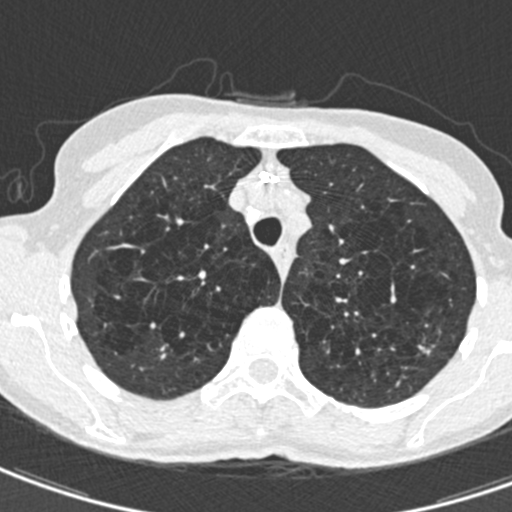
Chest CT (low-dose screening protocol), one axial image; second annual screen; lung window (W 1500 / L -600 HU); 0.75 mm slice thickness; standard (soft-tissue) reconstruction kernel (B30f); 512 × 512 image matrix. Female, age 71 years at enrolment. Current smoker at enrolment.
Expert-annotated lung lesion, bounding box [x1, y1, x2, y2] px = [403, 331, 445, 370]. The screening reader recorded 2 non-calcified nodules or masses ≥4 mm on this exam (right upper lobe, left upper lobe); which of them this box marks is not recorded. Participant outcome: lung cancer diagnosed 604 days after this screen (after the third annual screen) — adenocarcinoma, NOS, left upper lobe, moderately differentiated (G2), stage IA (AJCC 6th edition), 12 mm at pathology.